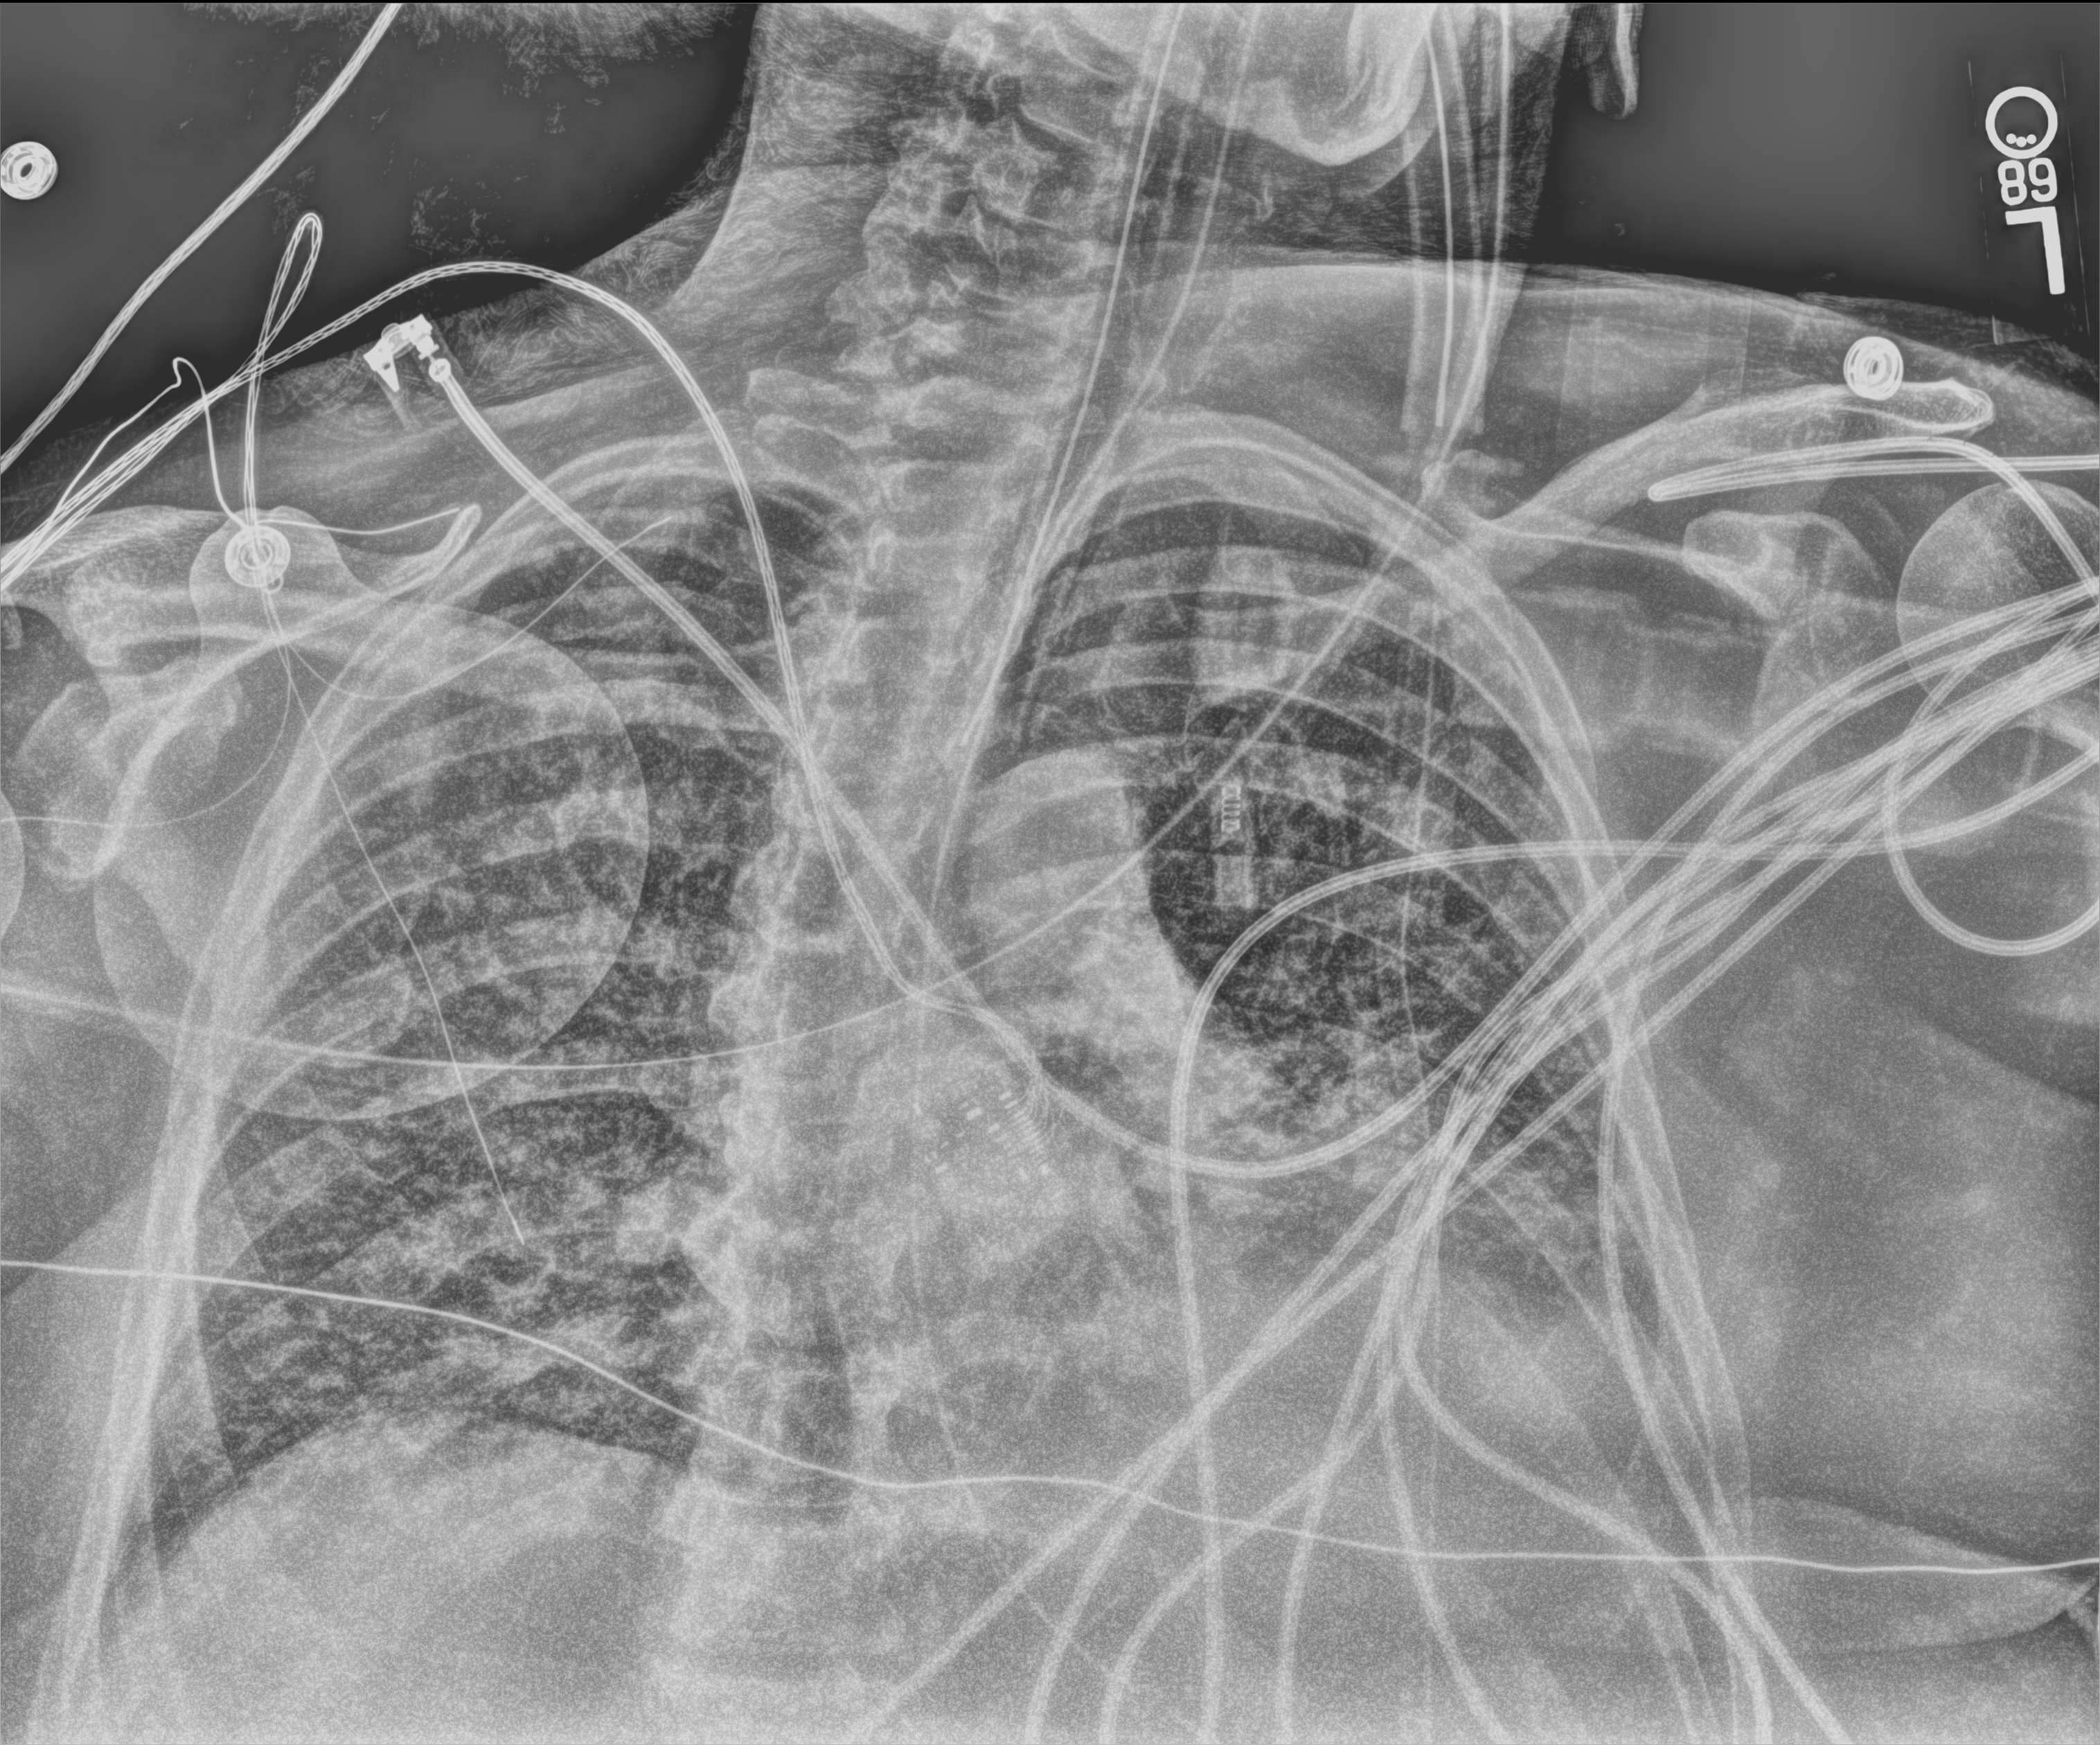
Portable chest radiograph, anteroposterior (AP) projection. Adult patient hospitalised with COVID-19, age 18–59 years.
Admission-level facts for this patient (not findings on this image; timing relative to this image not recorded):
- admitted to intensive care during this hospital stay: yes
- mechanically ventilated during this hospital stay: yes